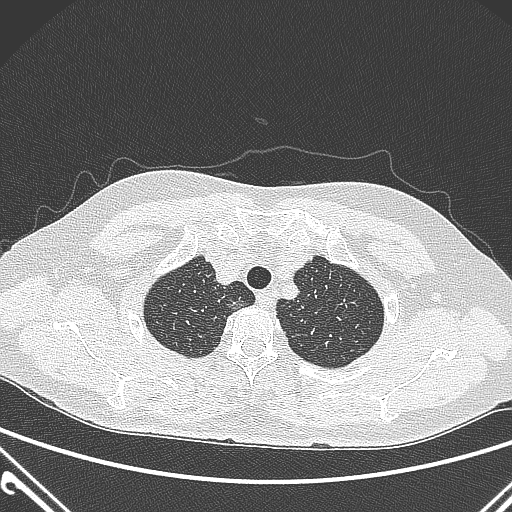
Chest CT, one axial slice. Position 246 of 300 along the scan axis. 120 kVp. Lung window (W 1500 / L -600 HU). 1 mm slice thickness. 512 × 512 image matrix. Patient: female, 54 years. From the clinical record (not read from this slice): clinical TNM (as recorded): T1a N0 M0.
Structures marked on this image (bounding box drawn by a radiologist):
- lung tumour (recorded histology: adenocarcinoma): box from (x=225, y=292) to (x=248, y=316) px